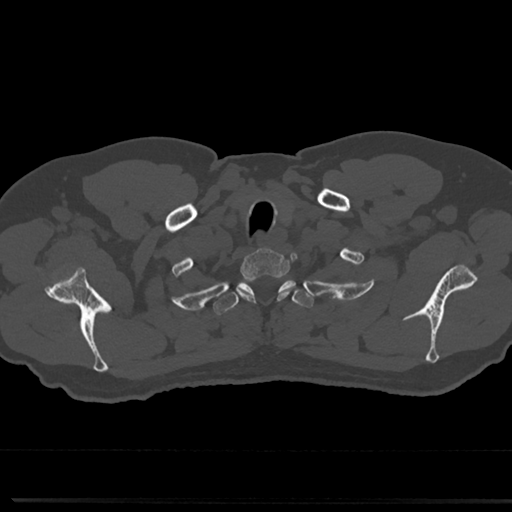
CT including the spine, one axial slice; slice 654 of 817 in the series (ordered by position); bone window (W 1800 / L 400 HU); 512 × 512 image matrix, field of view 355 × 355 mm. Patient: male, 61 years. From the clinical record (not read from this slice): primary cancer: prostate.
Annotated regions visible in this slice (semi-automatically segmented with operator editing):
- T1 vertebra: bounding box (x1, y1, x2, y2) in pixels: (240, 250, 288, 276)
- T2 vertebra: (221, 274, 308, 315)